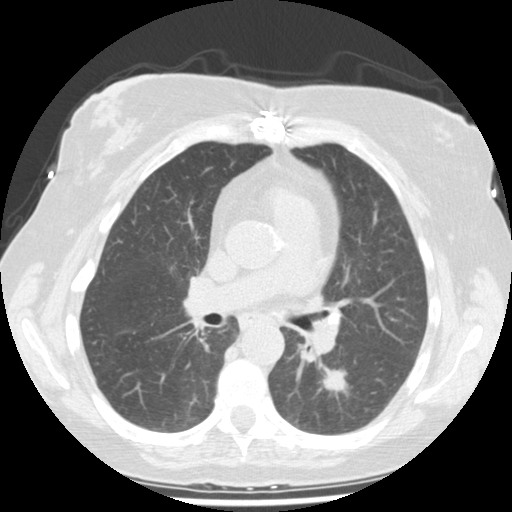
Chest CT (low-dose screening protocol), one axial image, second annual screen, lung window (W 1500 / L -600 HU), standard (soft-tissue) reconstruction kernel (STANDARD), 120 kVp. Female, age 61 years at enrolment. Current smoker at enrolment.
Expert reader's lesion annotation, box from (x=312, y=355) to (x=368, y=407) px. The screening reader recorded 2 non-calcified nodules or masses ≥4 mm on this exam (left lower lobe, right upper lobe); which of them this box marks is not recorded.